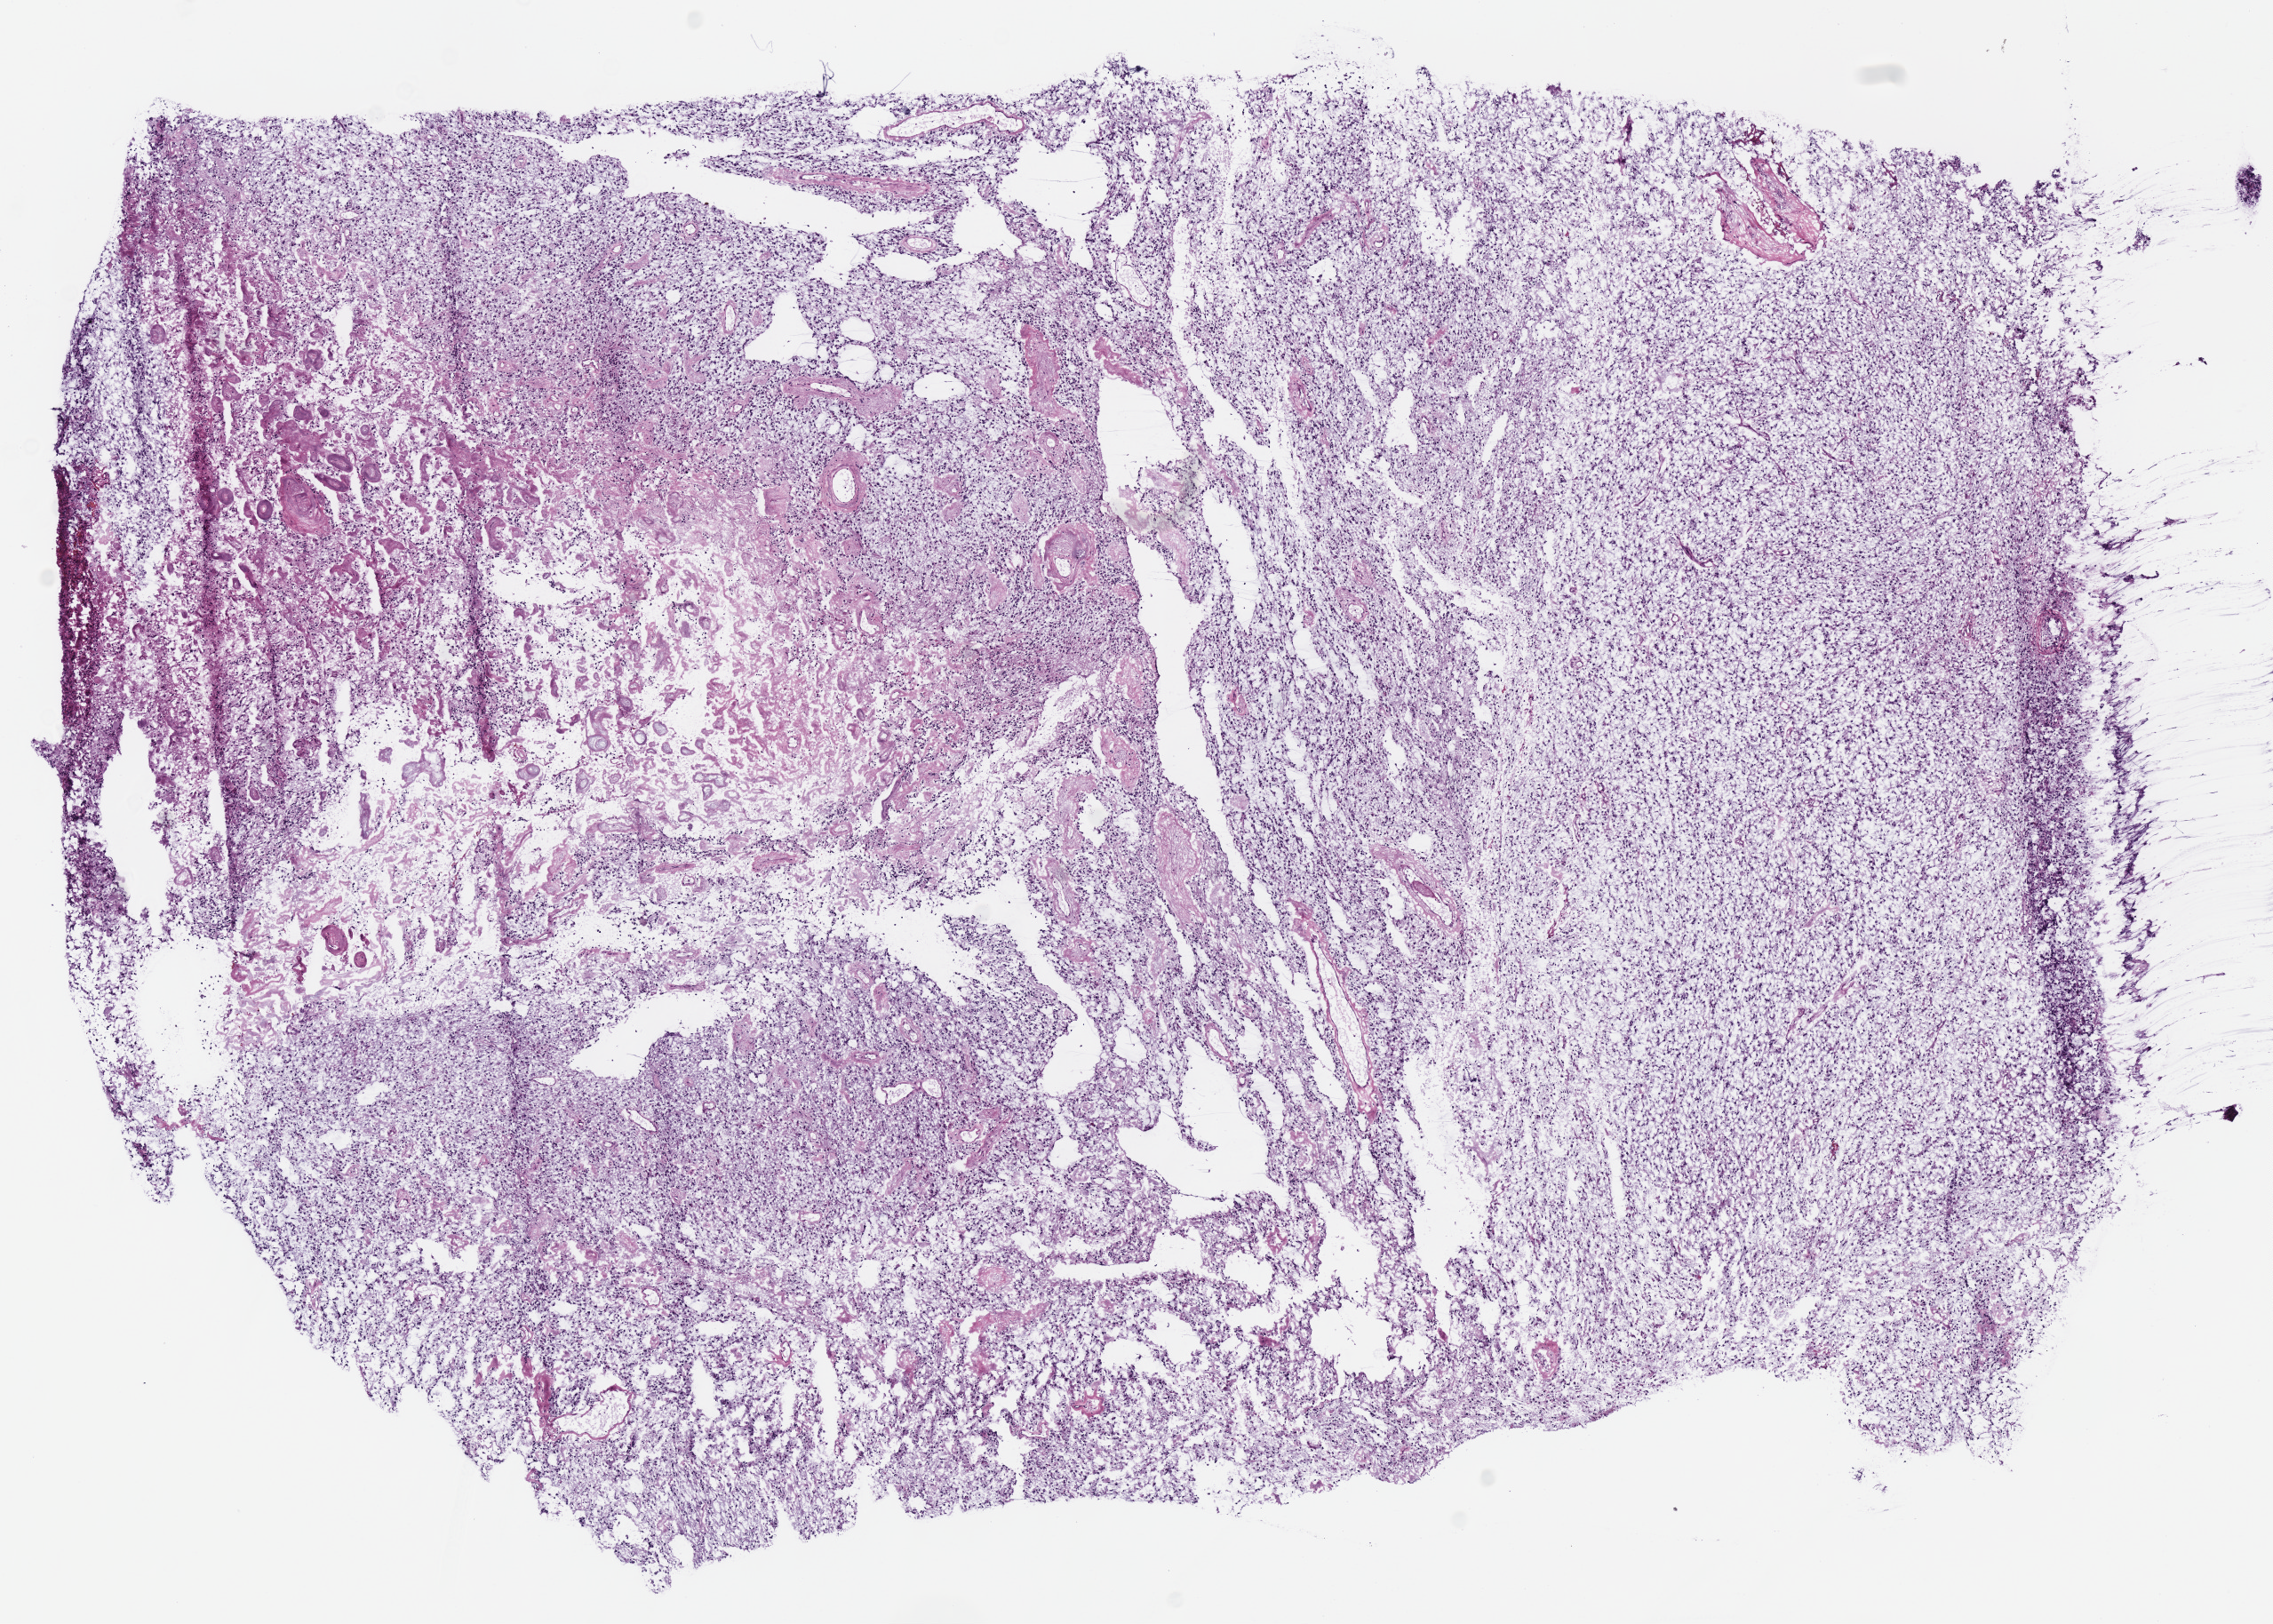
H&E whole-slide image — a low-resolution overview of the entire scanned area, about 10.1 x 7.2 mm (slide scanned at 40x); frozen section; brain, primary tumour sample. Female, age 51 years at initial diagnosis. Histologic grade: G2 (moderately differentiated). Composition of this section per pathologist review: tumour cells 85%, tumour nuclei 85%, normal cells 0%, stromal cells 15%, necrosis 0%.
Pathologic diagnosis: Oligodendroglioma, NOS (cerebrum).